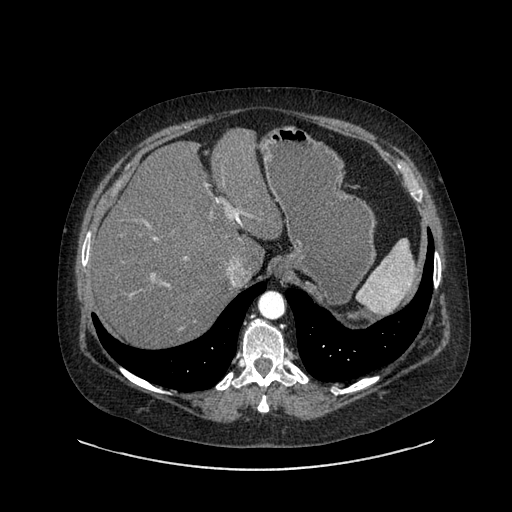
Contrast-enhanced abdominal CT, one axial slice; position 648 of 769 along the scan axis; reconstruction kernel SOFT; intravenous contrast given; soft-tissue window (W 400 / L 40 HU); 0.62 mm slice thickness; 512 × 512 image matrix, field of view 460 × 460 mm. Patient: female, 61 years. Case-level facts recorded for this patient, not image findings: diagnosis: adrenocortical carcinoma; tumour side: left adrenal; tumour size at pathology: 13 cm; Ki-67 index: 79 %; stage (as recorded): 2.
Outlined on this slice (semi-automatic segmentation, software-assisted and operator-edited):
- mass: bounding box <342,309,363,327> (left, top, right, bottom; pixels)